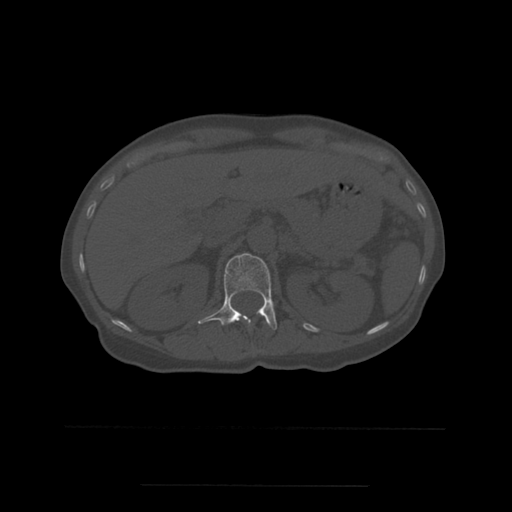
CT including the spine, one axial slice. Position 240 of 544 along the scan axis. Bone window (W 1800 / L 400 HU). 1.25 mm slice thickness. 512 × 512 image matrix, field of view 350 × 350 mm. Patient age 58 years. Case-level facts recorded for this patient, not image findings: primary cancer: lung.
Annotated regions visible in this slice (semi-automatic segmentation, software-assisted and operator-edited):
- L1 vertebra: bounding box (x1, y1, x2, y2) in pixels: (198, 253, 277, 330)